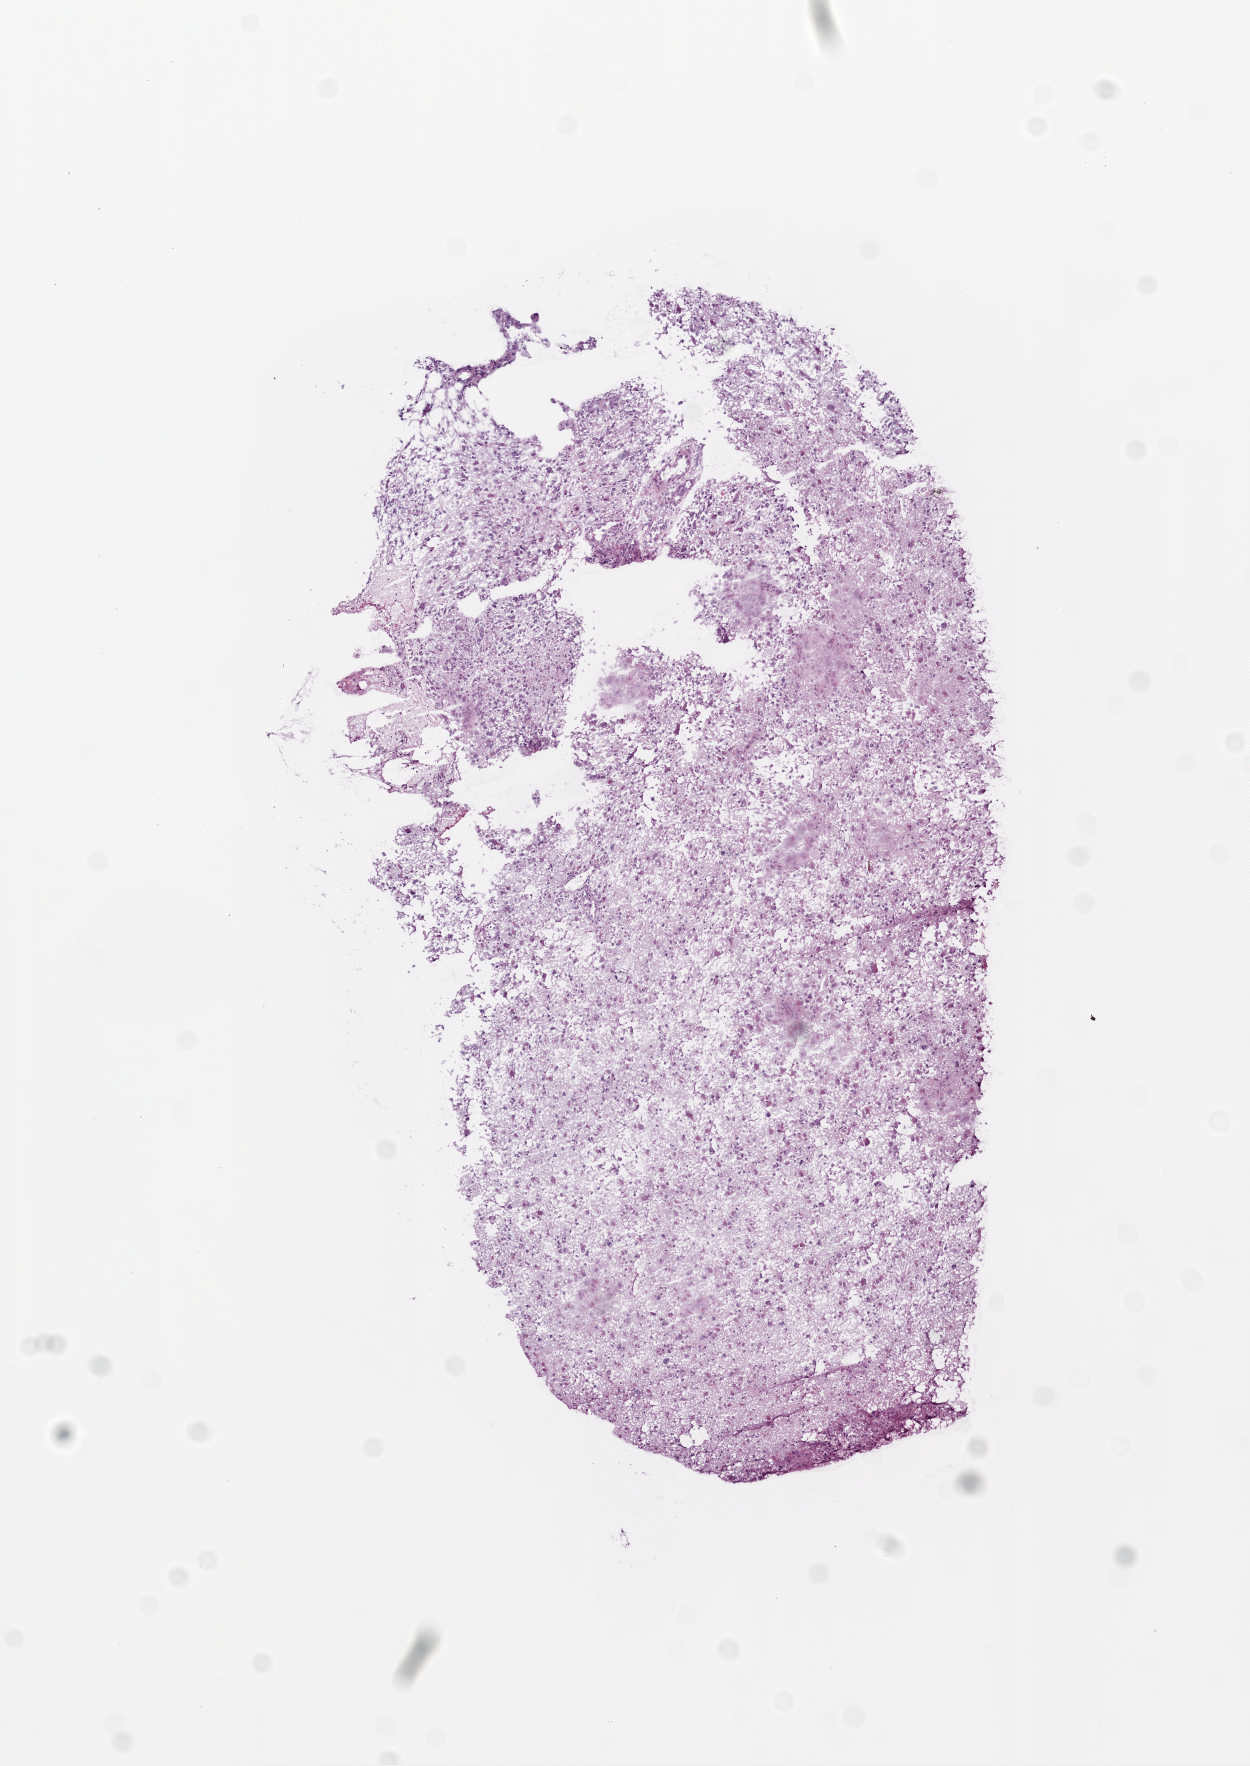
Whole-slide histology image, Hematoxylin and eosin (H&E) stained, low-resolution overview of the scanned area, about 5.0 x 7.1 mm, frozen section from the top of the tissue portion, sample: primary tumour, brain. Male, age 63 years at initial diagnosis. Pathologist review of this section (percent, as recorded): tumour cells 95%, tumour nuclei 80%, normal cells 0%, stromal cells 0%, necrosis 5%.
- histologic diagnosis: Glioblastoma